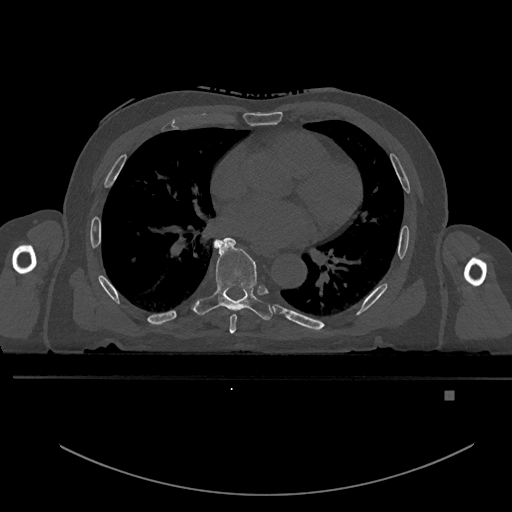
CT including the spine, one axial slice; slice 264 of 969 in the series (ordered by position); bone window (W 1800 / L 400 HU); 0.5 mm slice thickness; 512 × 512 image matrix, field of view 456 × 456 mm. Male patient, age 82 years. From the clinical record (not read from this slice): primary cancer: prostate.
Outlined on this slice (semi-automatically segmented with operator editing):
- T6 vertebra: box from (x=229, y=314) to (x=237, y=334) px
- T7 vertebra: (x=192, y=237)–(x=273, y=321)